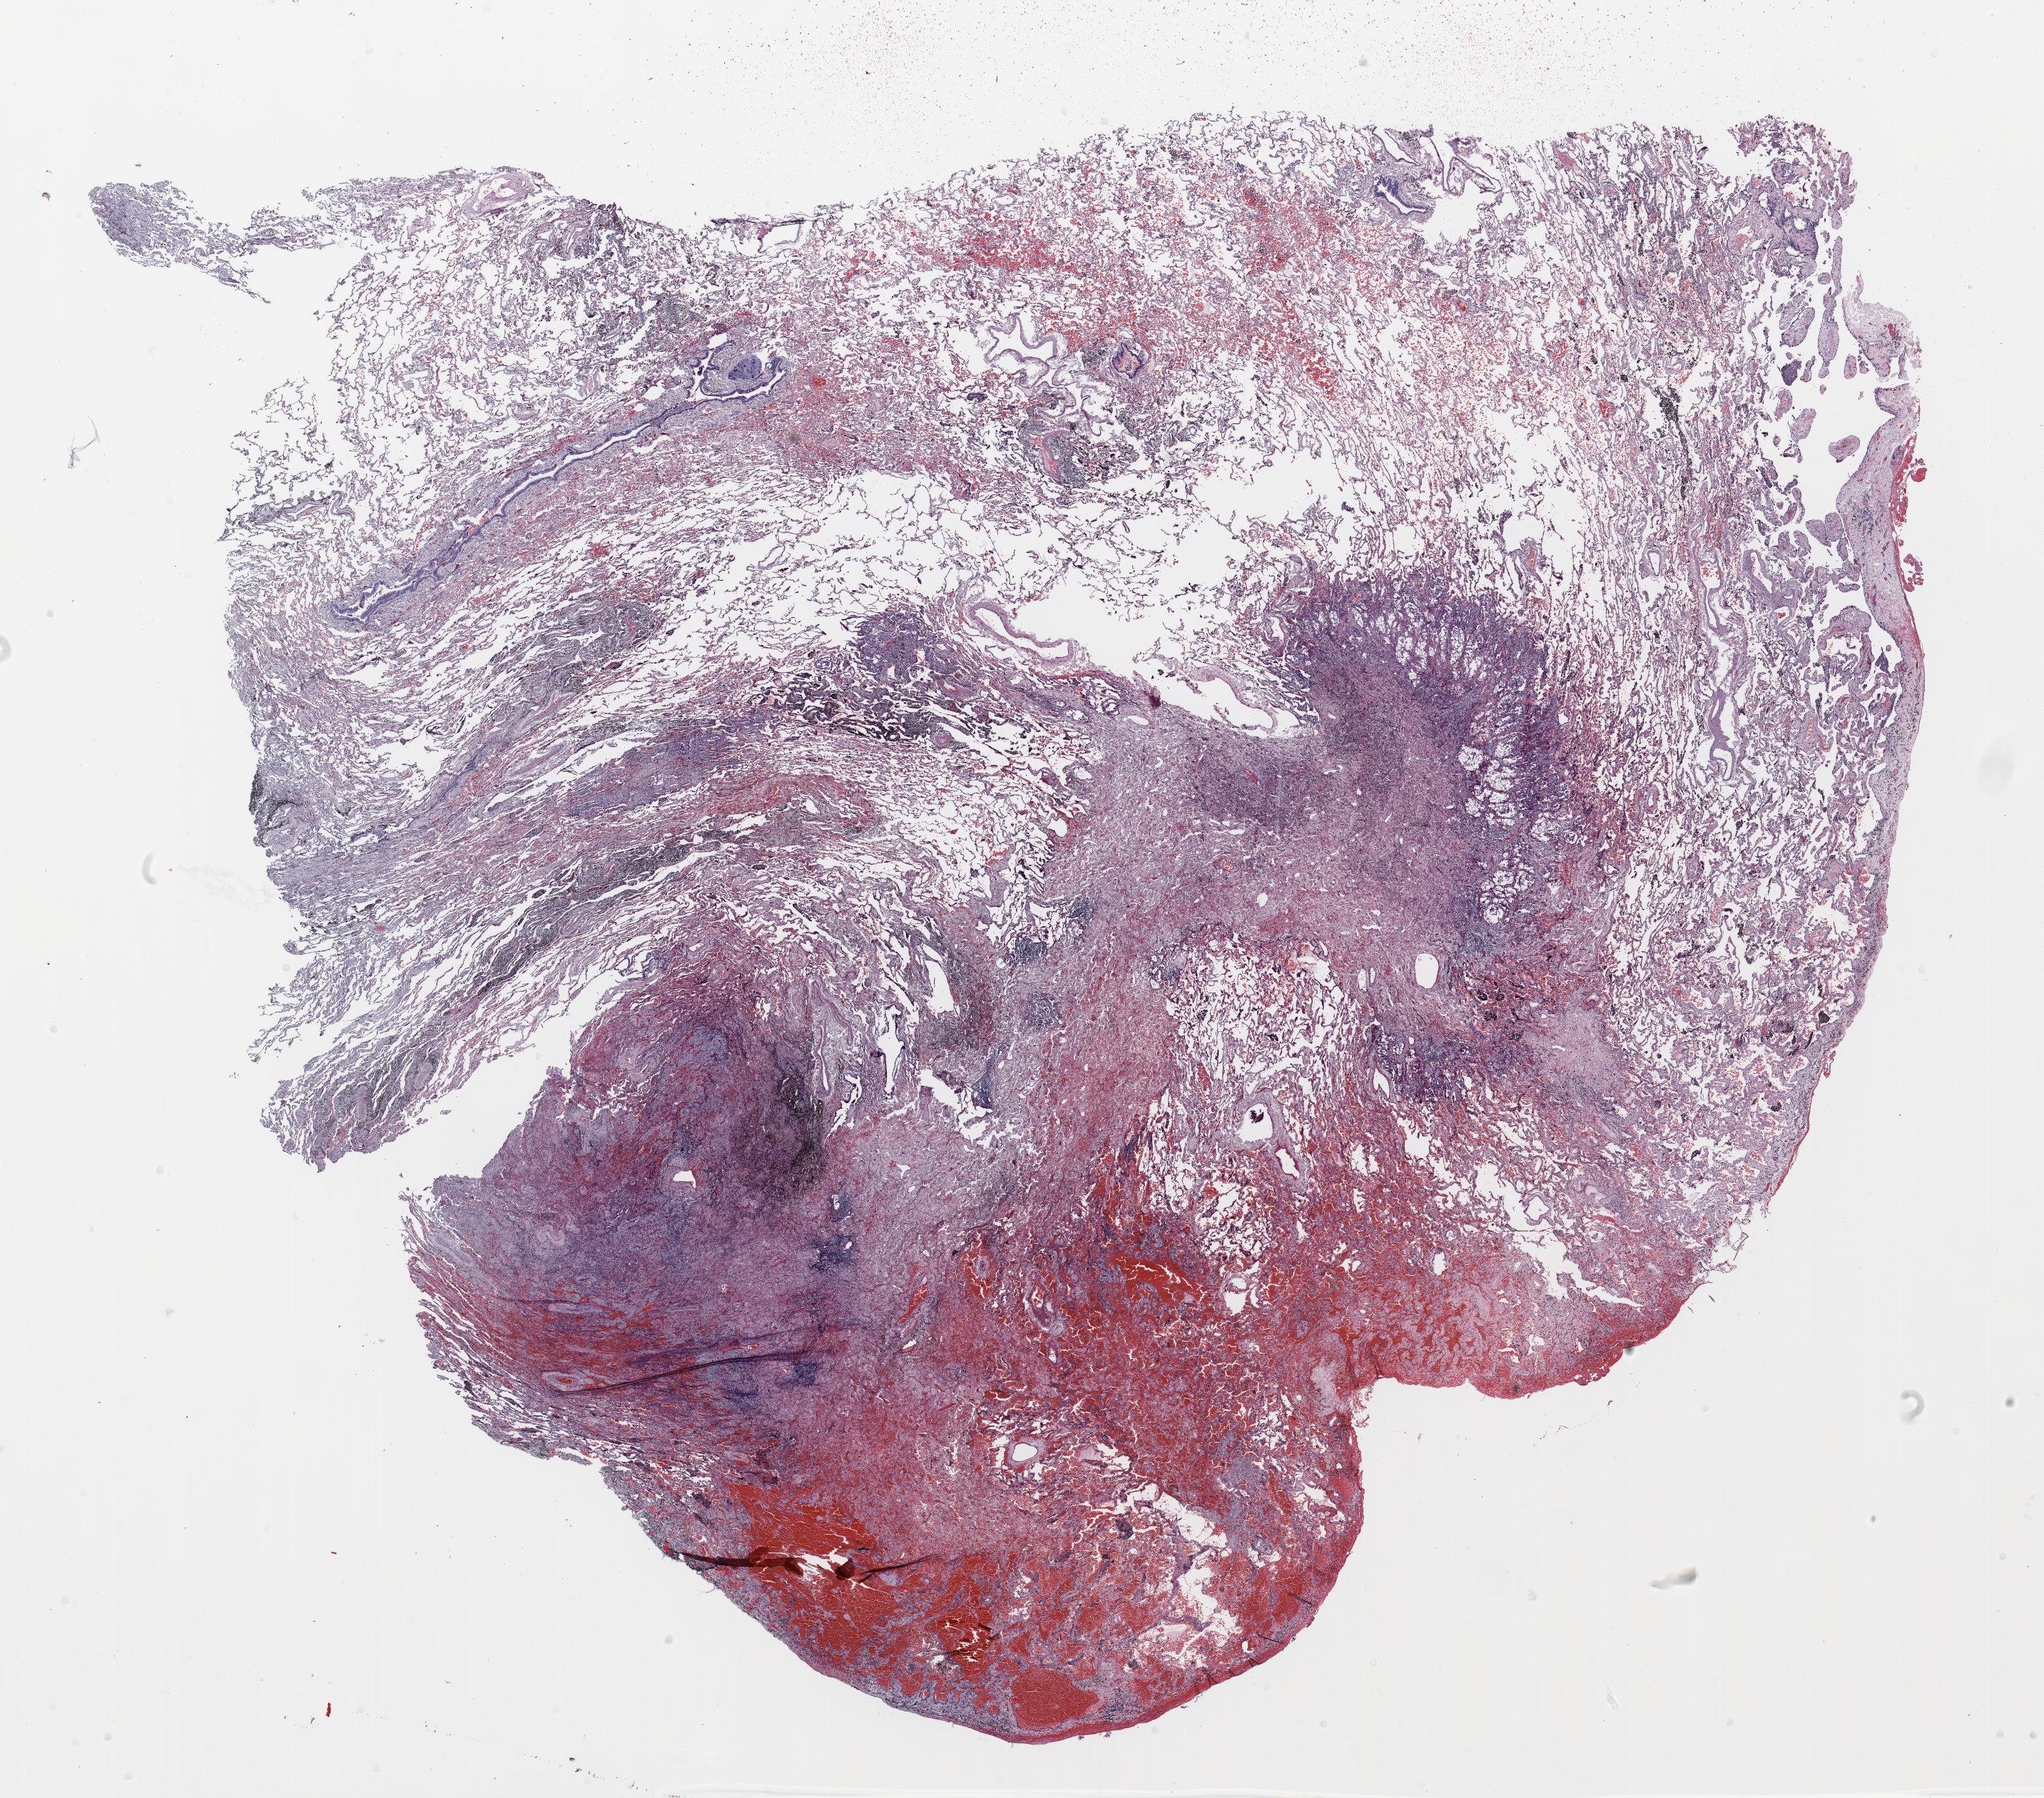
Whole-slide histology image, Hematoxylin and eosin (H&E) stained — low-resolution overview of the scanned area, about 23.0 x 20.3 mm (from a 20x scan). Formalin-fixed paraffin-embedded (FFPE) section. Lung tissue. Male, age 63 at enrolment. Current smoker at enrolment. Grade: moderately differentiated (G2).
* primary tumour location (clinical record): right upper lobe
* stage (AJCC 6th edition): IA
* tumour size (pathology): 15 mm
* participant's lung-cancer diagnosis: Bronchiolo-alveolar adenocarcinoma, NOS (ICD-O-3 8250/3)
* ICD-O-3 topography: upper lobe of lung (C34.1)